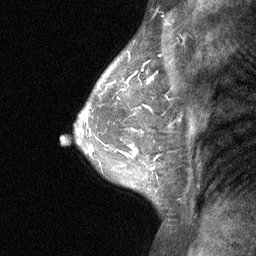
Breast MRI (dynamic contrast-enhanced), one sagittal slice. Slice 45 of 64 in the series (ordered by position). Dynamic contrast-enhanced study with each time point stored as its own series, time point 2 of 3 at this slice position (early post-contrast, ordered by acquisition time). 1.5 T. TE 4.8 ms, TR 27 ms. 256 × 256 image matrix. Patient: female, 47 years. Case-level facts recorded for this patient, not image findings: setting: breast cancer imaged before/during neoadjuvant chemotherapy; receptor status: HR-positive, HER2-negative.
Outlined on this slice (semi-automatic segmentation, software-assisted and operator-edited):
- analysis volume of interest (the breast-tissue region the enhancement analysis was run in; not a lesion): box from (x=104, y=138) to (x=165, y=198) px
- tumour enhancement mask (voxels above the 90 % enhancement threshold inside the analysis volume of interest): (x=134, y=150)–(x=155, y=169)